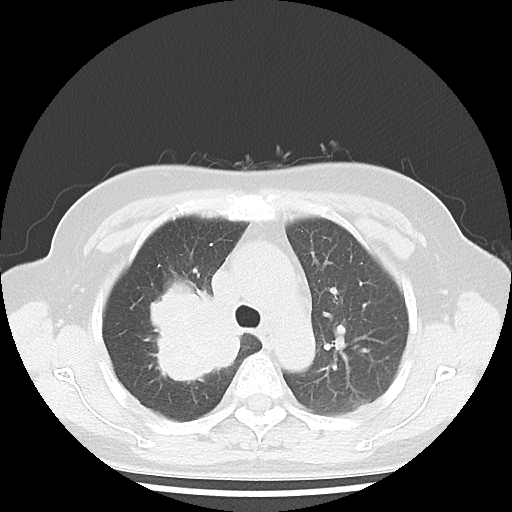
Chest CT, one axial slice; slice 30 of 43 in the series (ordered by position); reconstruction kernel LUNG; 100 kVp; lung window (W 1500 / L -600 HU); 5 mm slice thickness; 512 × 512 image matrix. Female patient, age 62 years. Case-level facts recorded for this patient, not image findings: clinical TNM (as recorded): T3 N0 M0; histopathological grade: G3.
Outlined on this slice (bounding box drawn by a radiologist):
- lung tumour (recorded histology: small cell carcinoma): bounding box (x1, y1, x2, y2) in pixels: (129, 271, 250, 391)